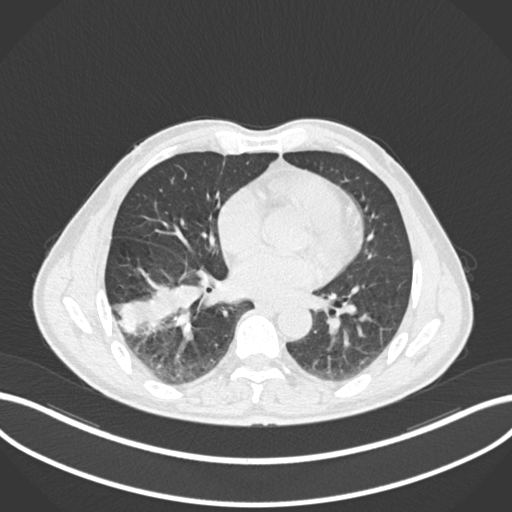
Chest CT, one axial slice. Slice 82 of 208 in the series (ordered by position). Reconstruction kernel B30f. 120 kVp. Lung window (W 1500 / L -600 HU). 512 × 512 image matrix, field of view 400 × 400 mm. Male patient, age 58 years. From the clinical record (not read from this slice): clinical TNM (as recorded): T3 N0 M0.
Outlined on this slice (rectangle marked by the reading radiologist):
- lung tumour (recorded histology: squamous cell carcinoma): bounding box [x1, y1, x2, y2] px = [117, 272, 200, 337]